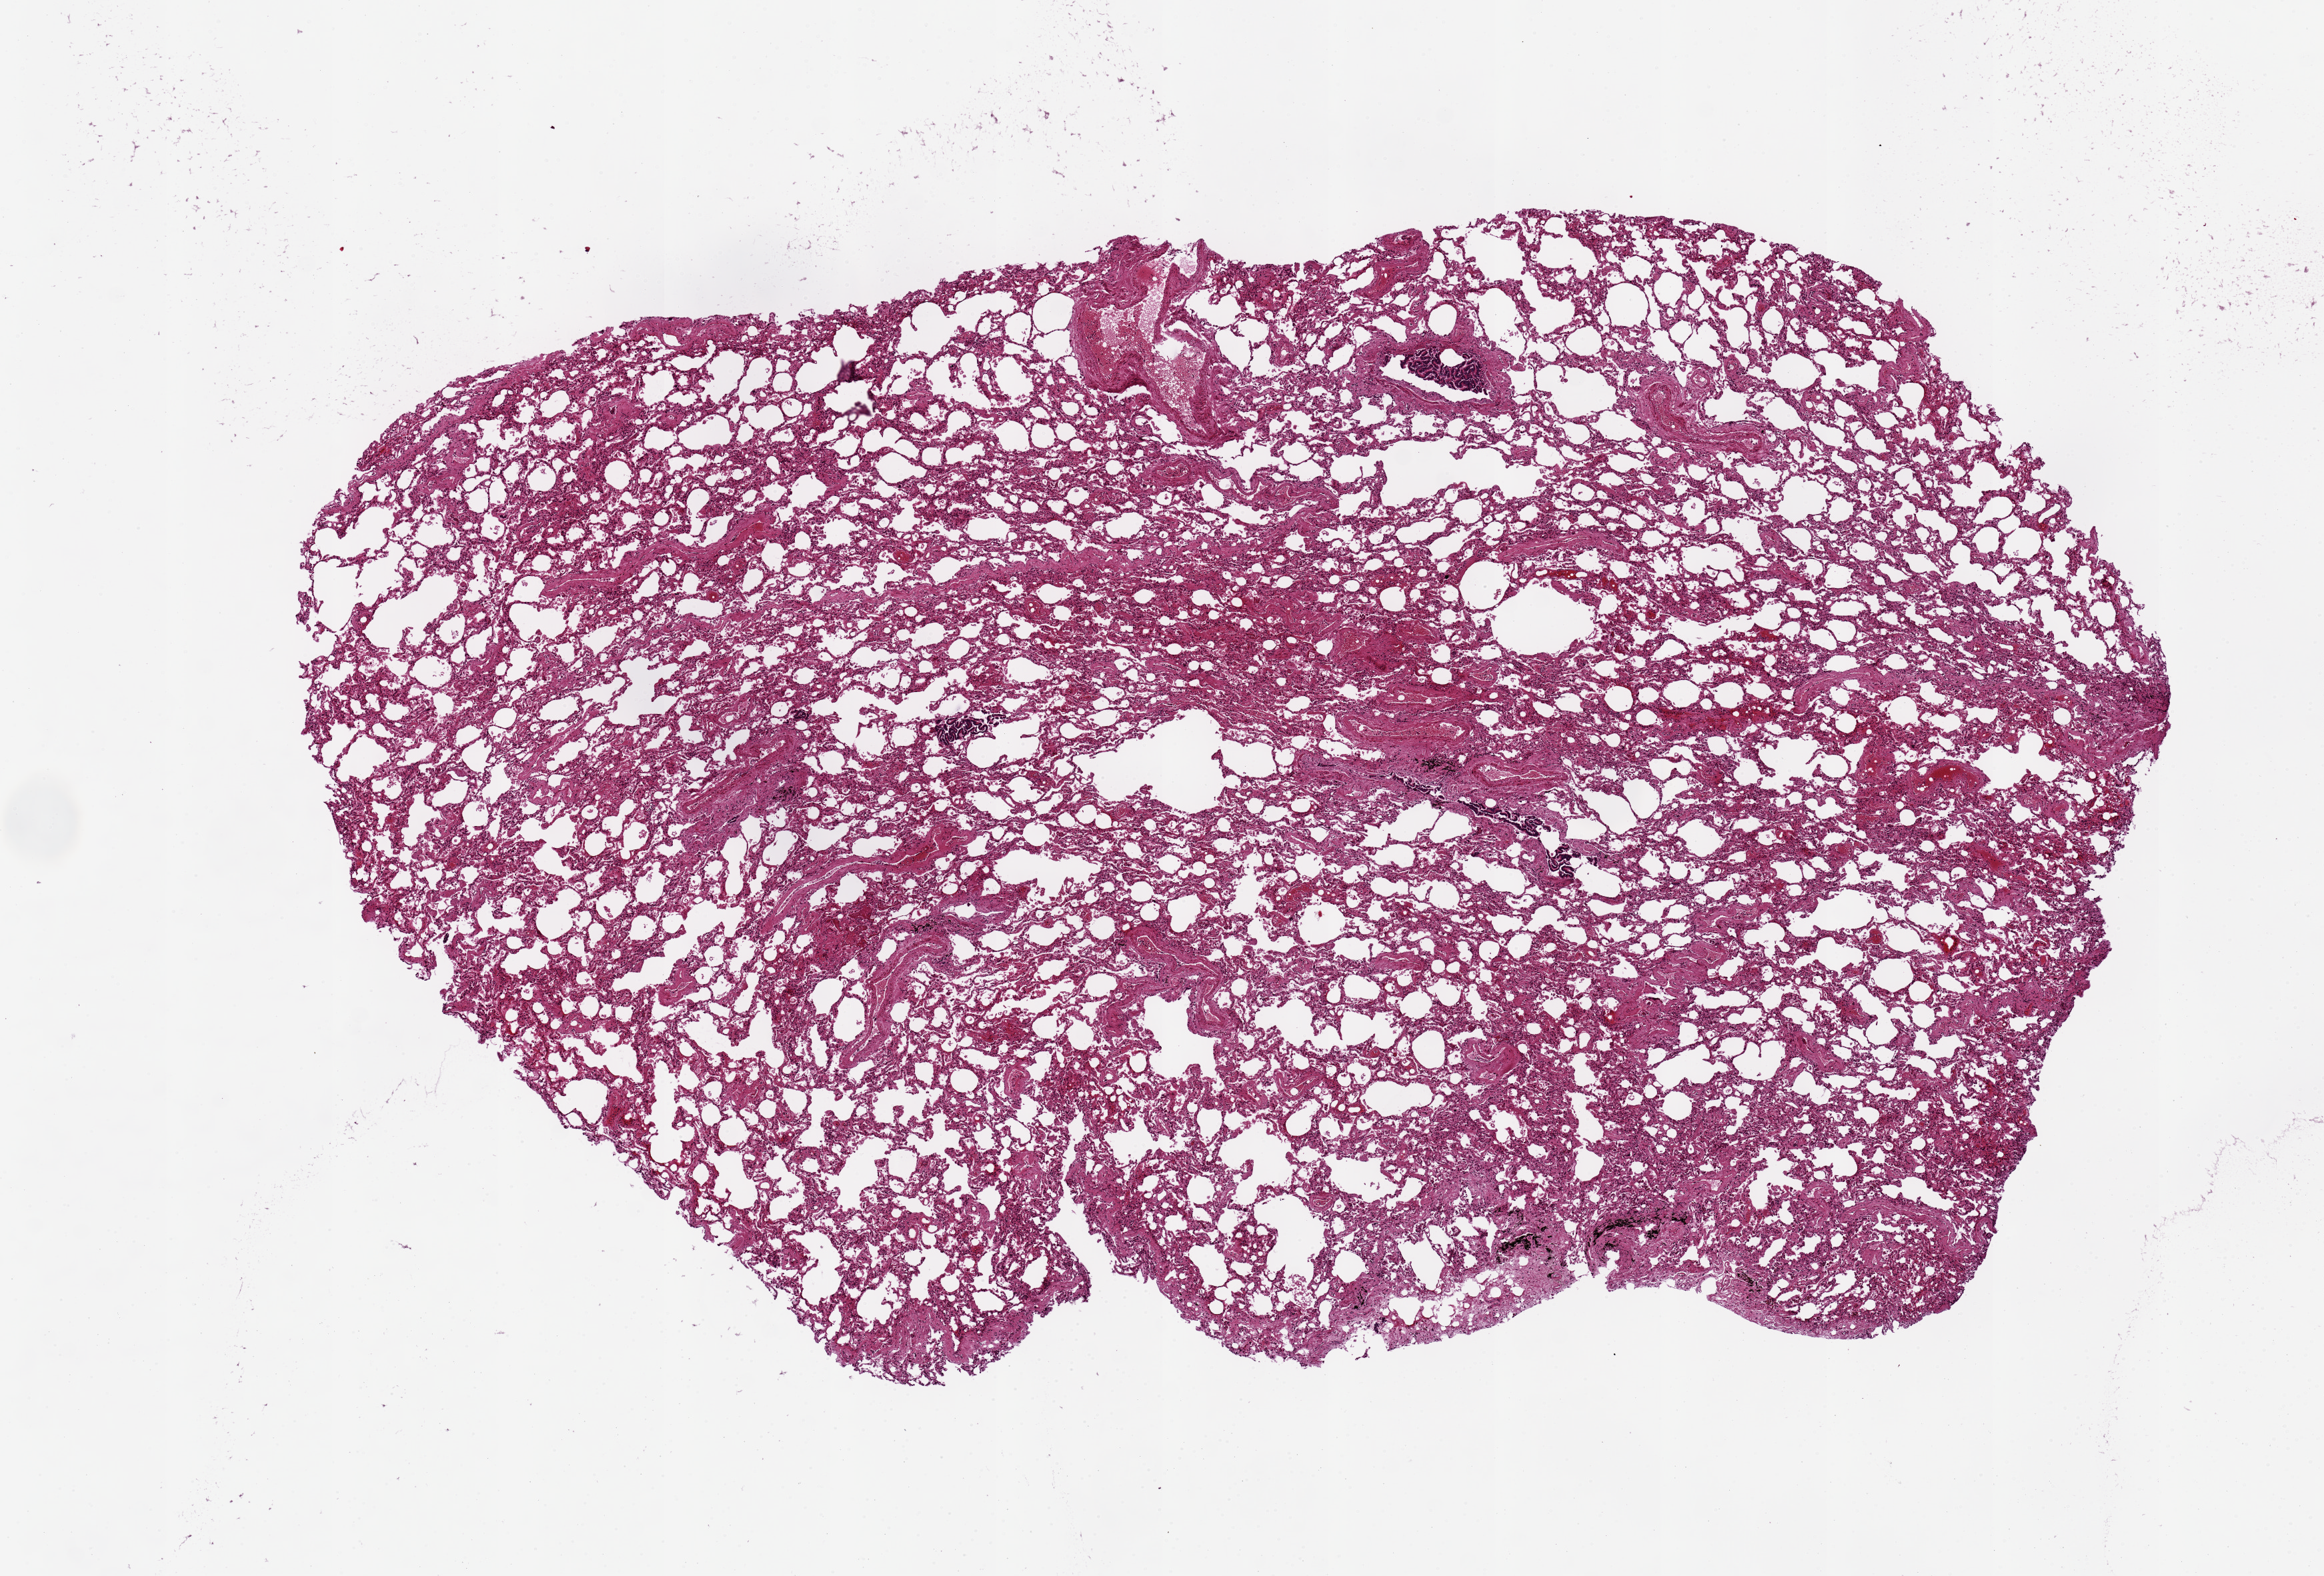
Whole-slide image, H&E stain, brightfield, shown as a low-resolution overview of the whole scanned area (about 13.8 x 9.3 mm), PAXgene-fixed, paraffin-embedded tissue, target tissue: lung, donor tissue sample. Male donor.
Pathologist's review note for this sample: Mild fibrosis and congestion. 11x6.6mm.